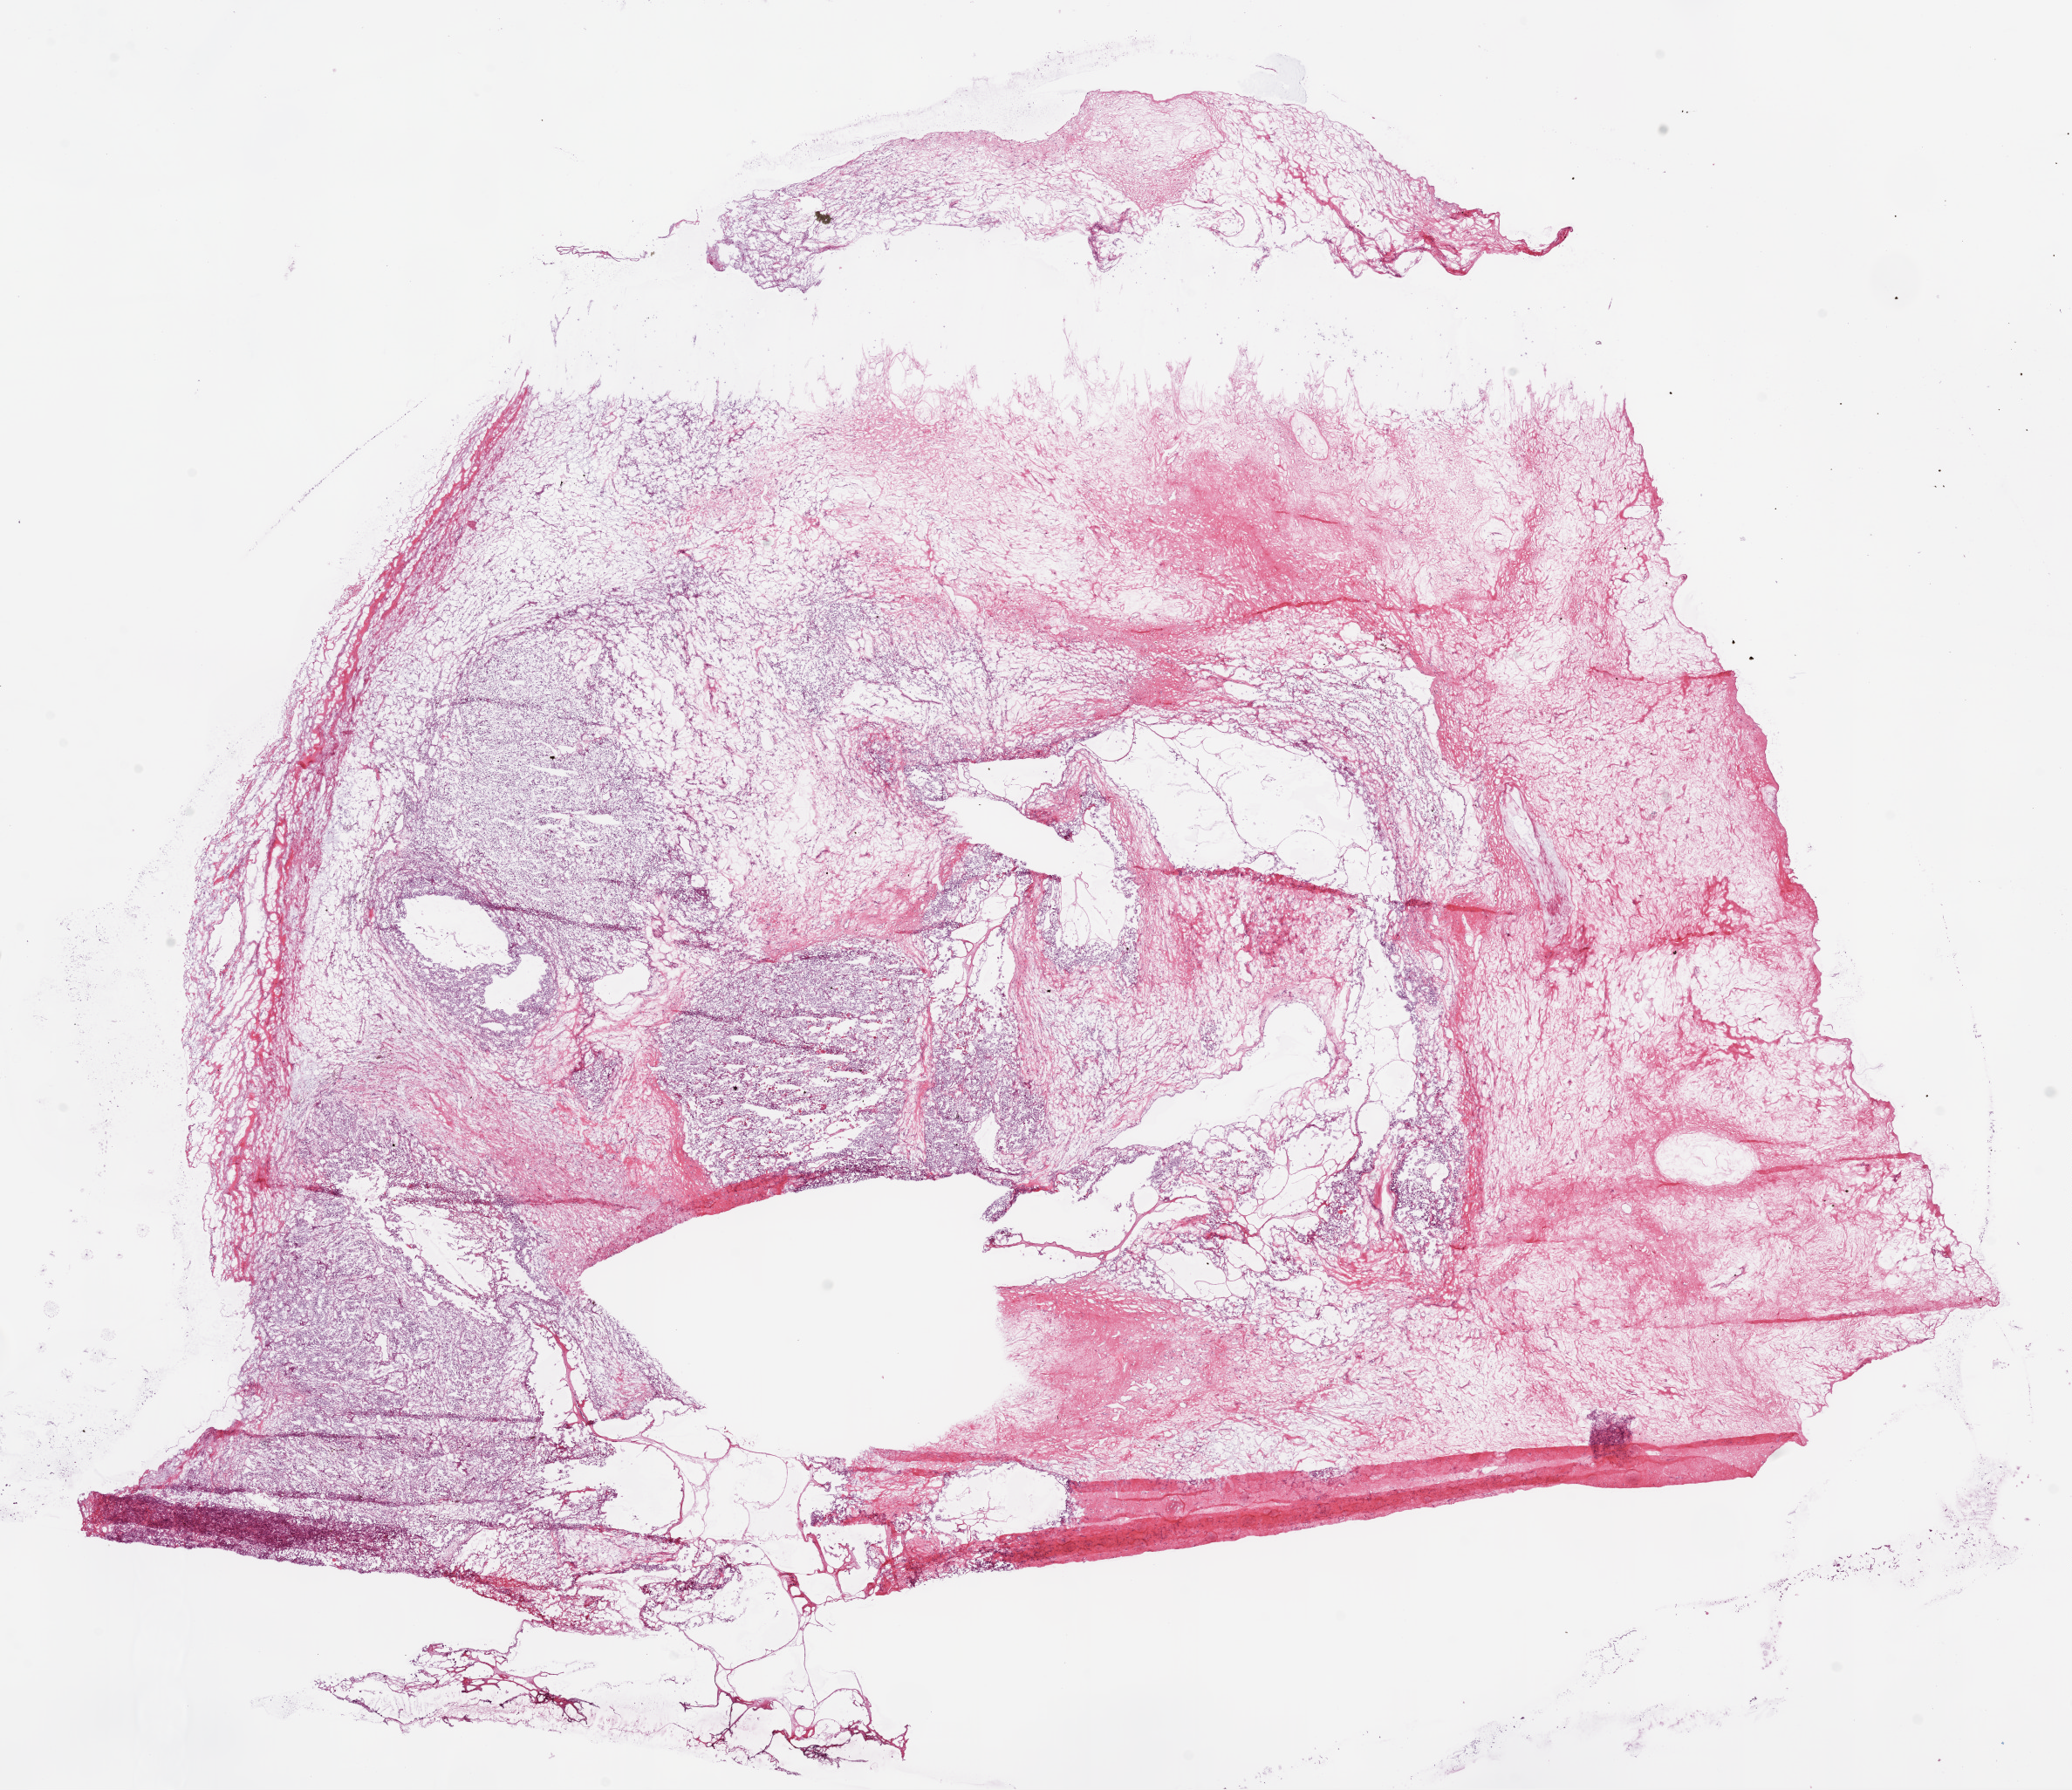
Digitized H&E tissue section (whole slide) — a low-resolution overview of the entire scanned area, about 19.1 x 16.5 mm (from a 20x scan). Frozen section from the bottom of the tissue portion. Primary tumour sample from the kidney. Patient: female, age at initial diagnosis 59 years. Histologic grade: G2 (moderately differentiated). Composition of this section per pathologist review: tumour cells 60%, tumour nuclei 80%, normal cells 0%, stromal cells 40%, necrosis 0%.
AJCC pathologic stage: III. Histologic diagnosis: Clear cell adenocarcinoma, NOS. Laterality: right.